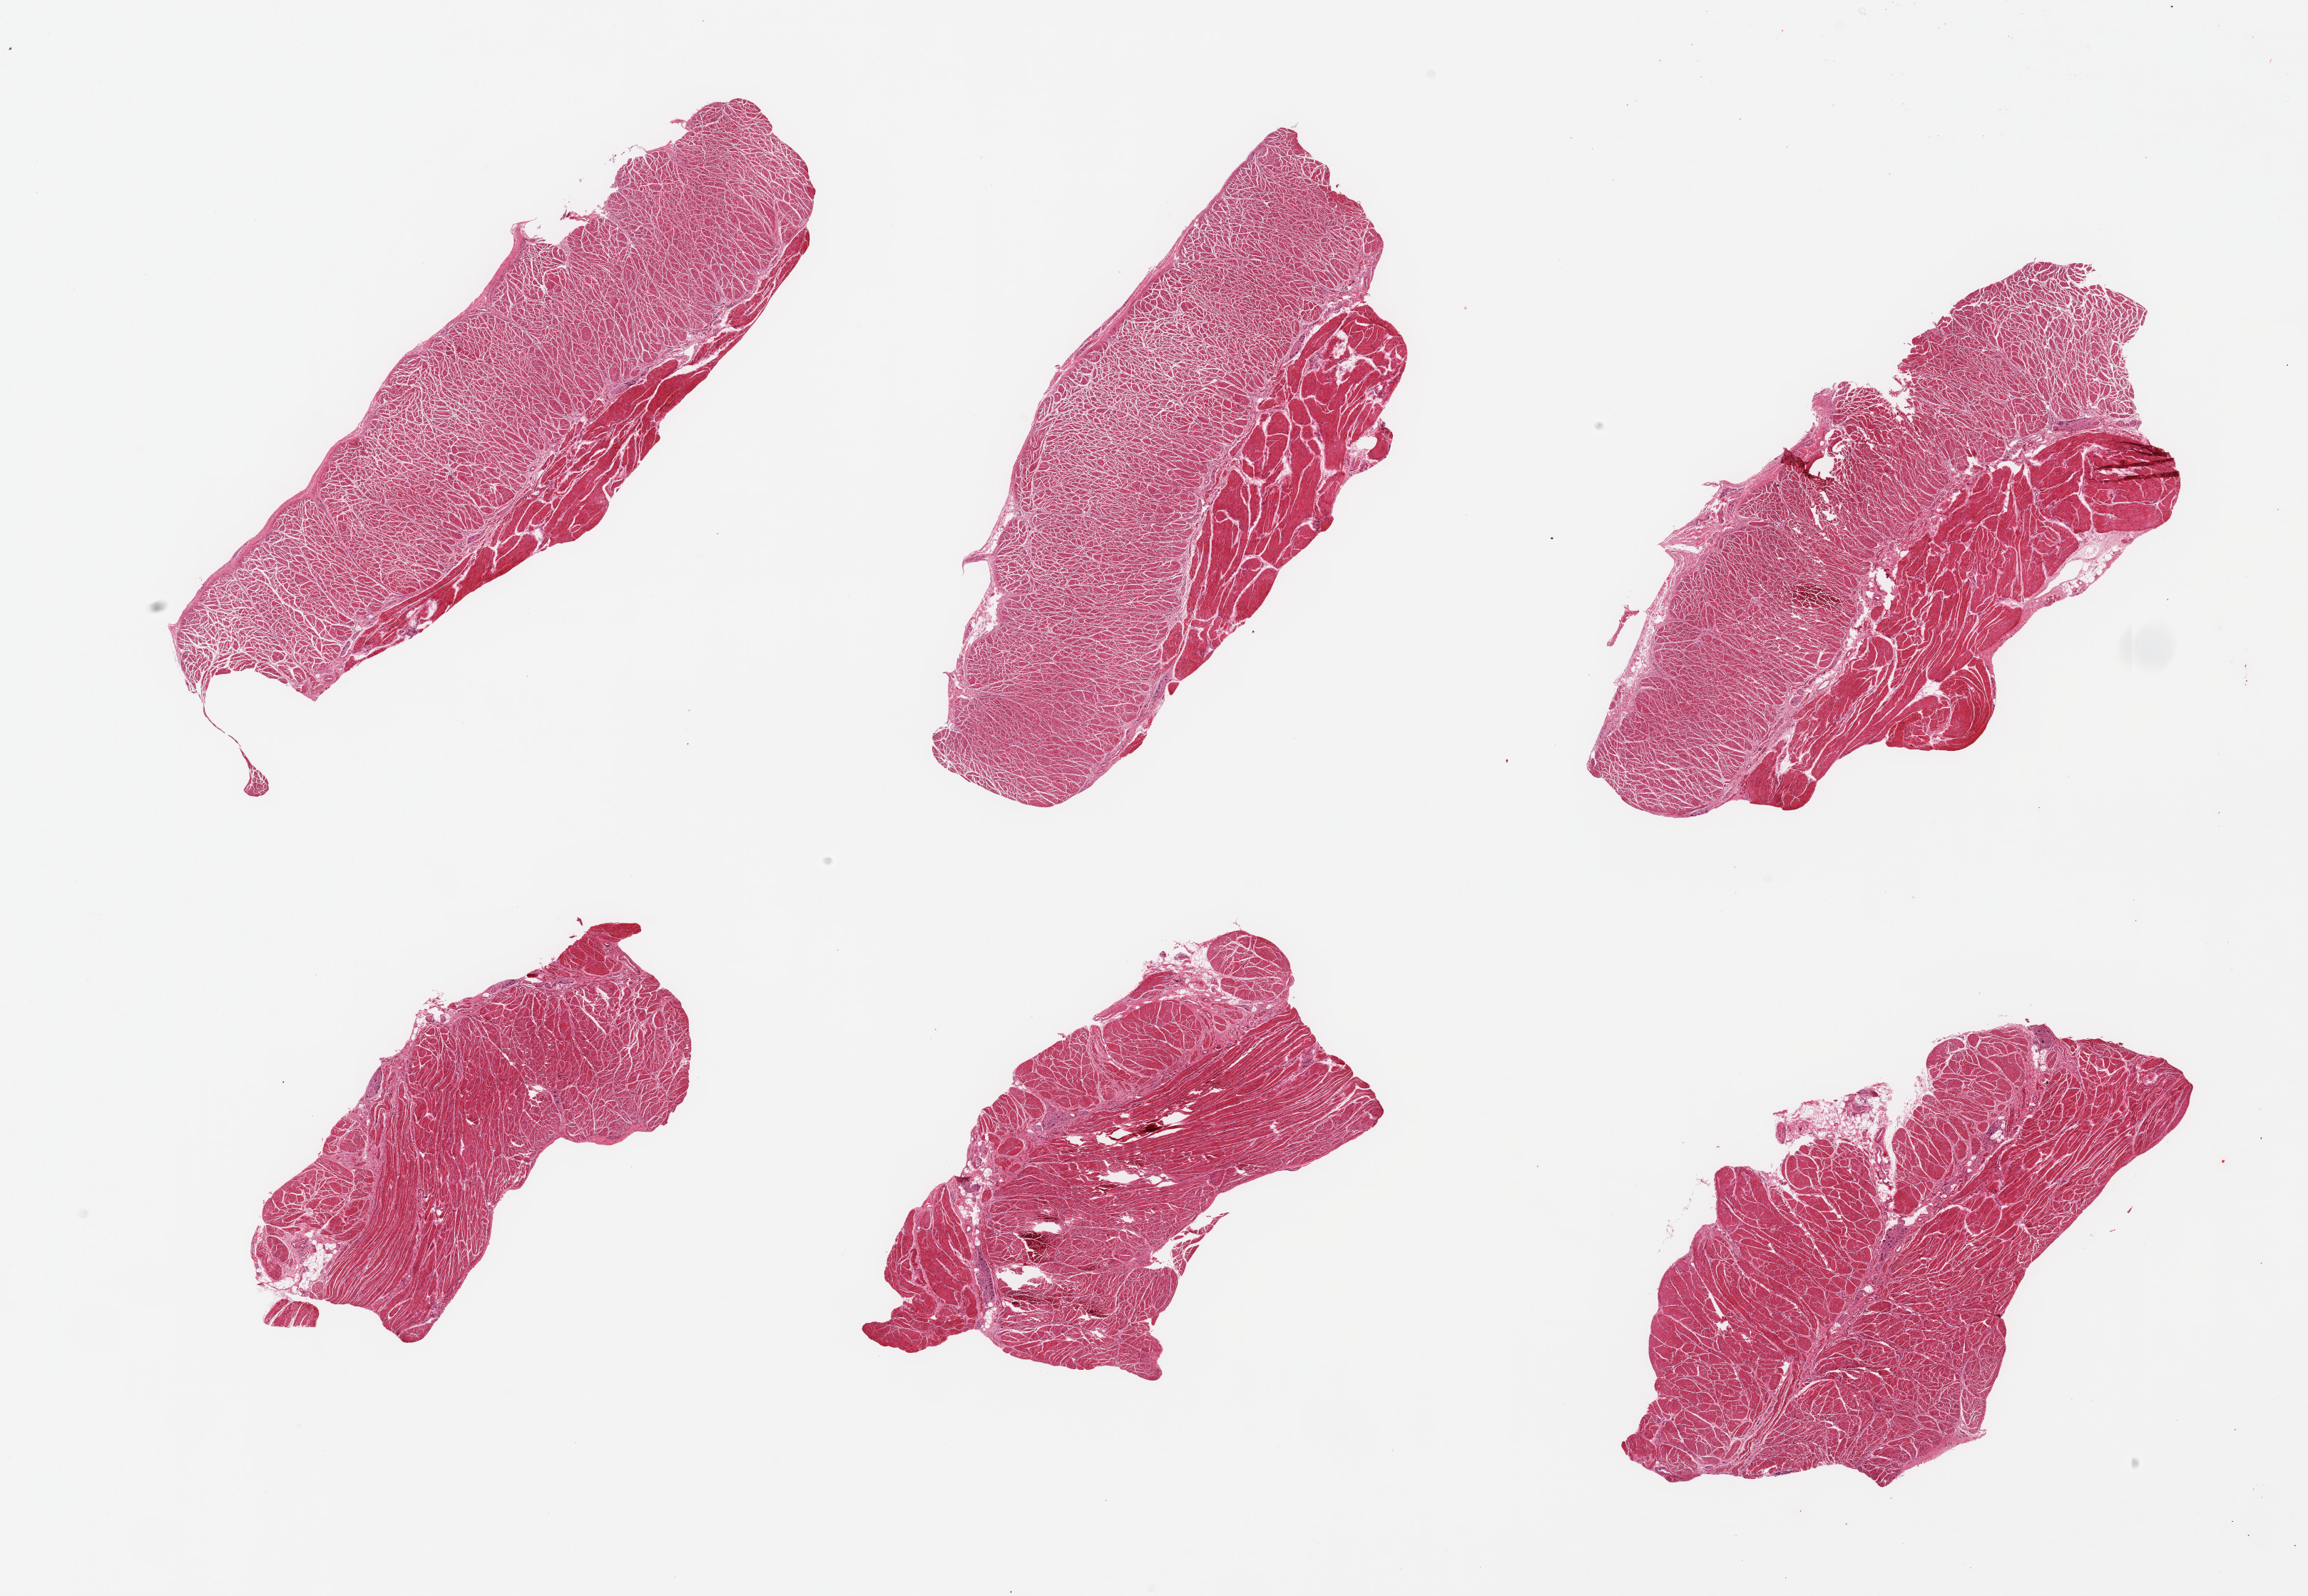
H&E whole-slide image — shown as a low-resolution overview of the whole scanned area (about 25.6 x 17.7 mm); PAXgene-fixed paraffin-embedded (PFPE) section; sampled site (target tissue): gastroesophageal junction; donor tissue sample.
* review note (as recorded): 6 pieces; well dissected muscle; well preserved ganglion cells